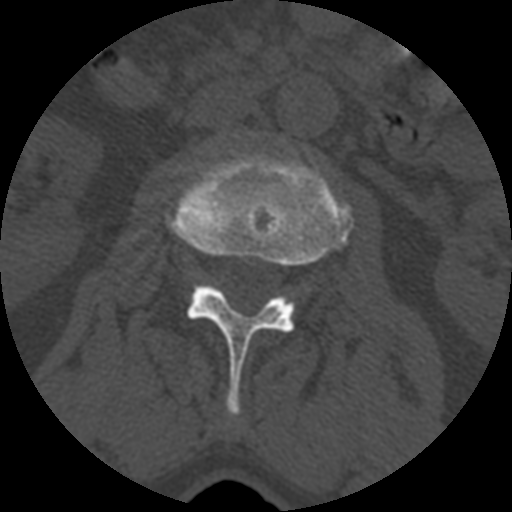
CT including the spine, one axial slice. Position 329 of 399 along the scan axis. Reconstruction kernel STANDARD. 120 kVp. Bone window (W 1800 / L 400 HU). 512 × 512 image matrix. Patient age 71 years. Case-level facts recorded for this patient, not image findings: primary cancer: prostate.
Outlined on this slice (semi-automatic segmentation, software-assisted and operator-edited):
- L2 vertebra: box from (x=167, y=155) to (x=352, y=417) px